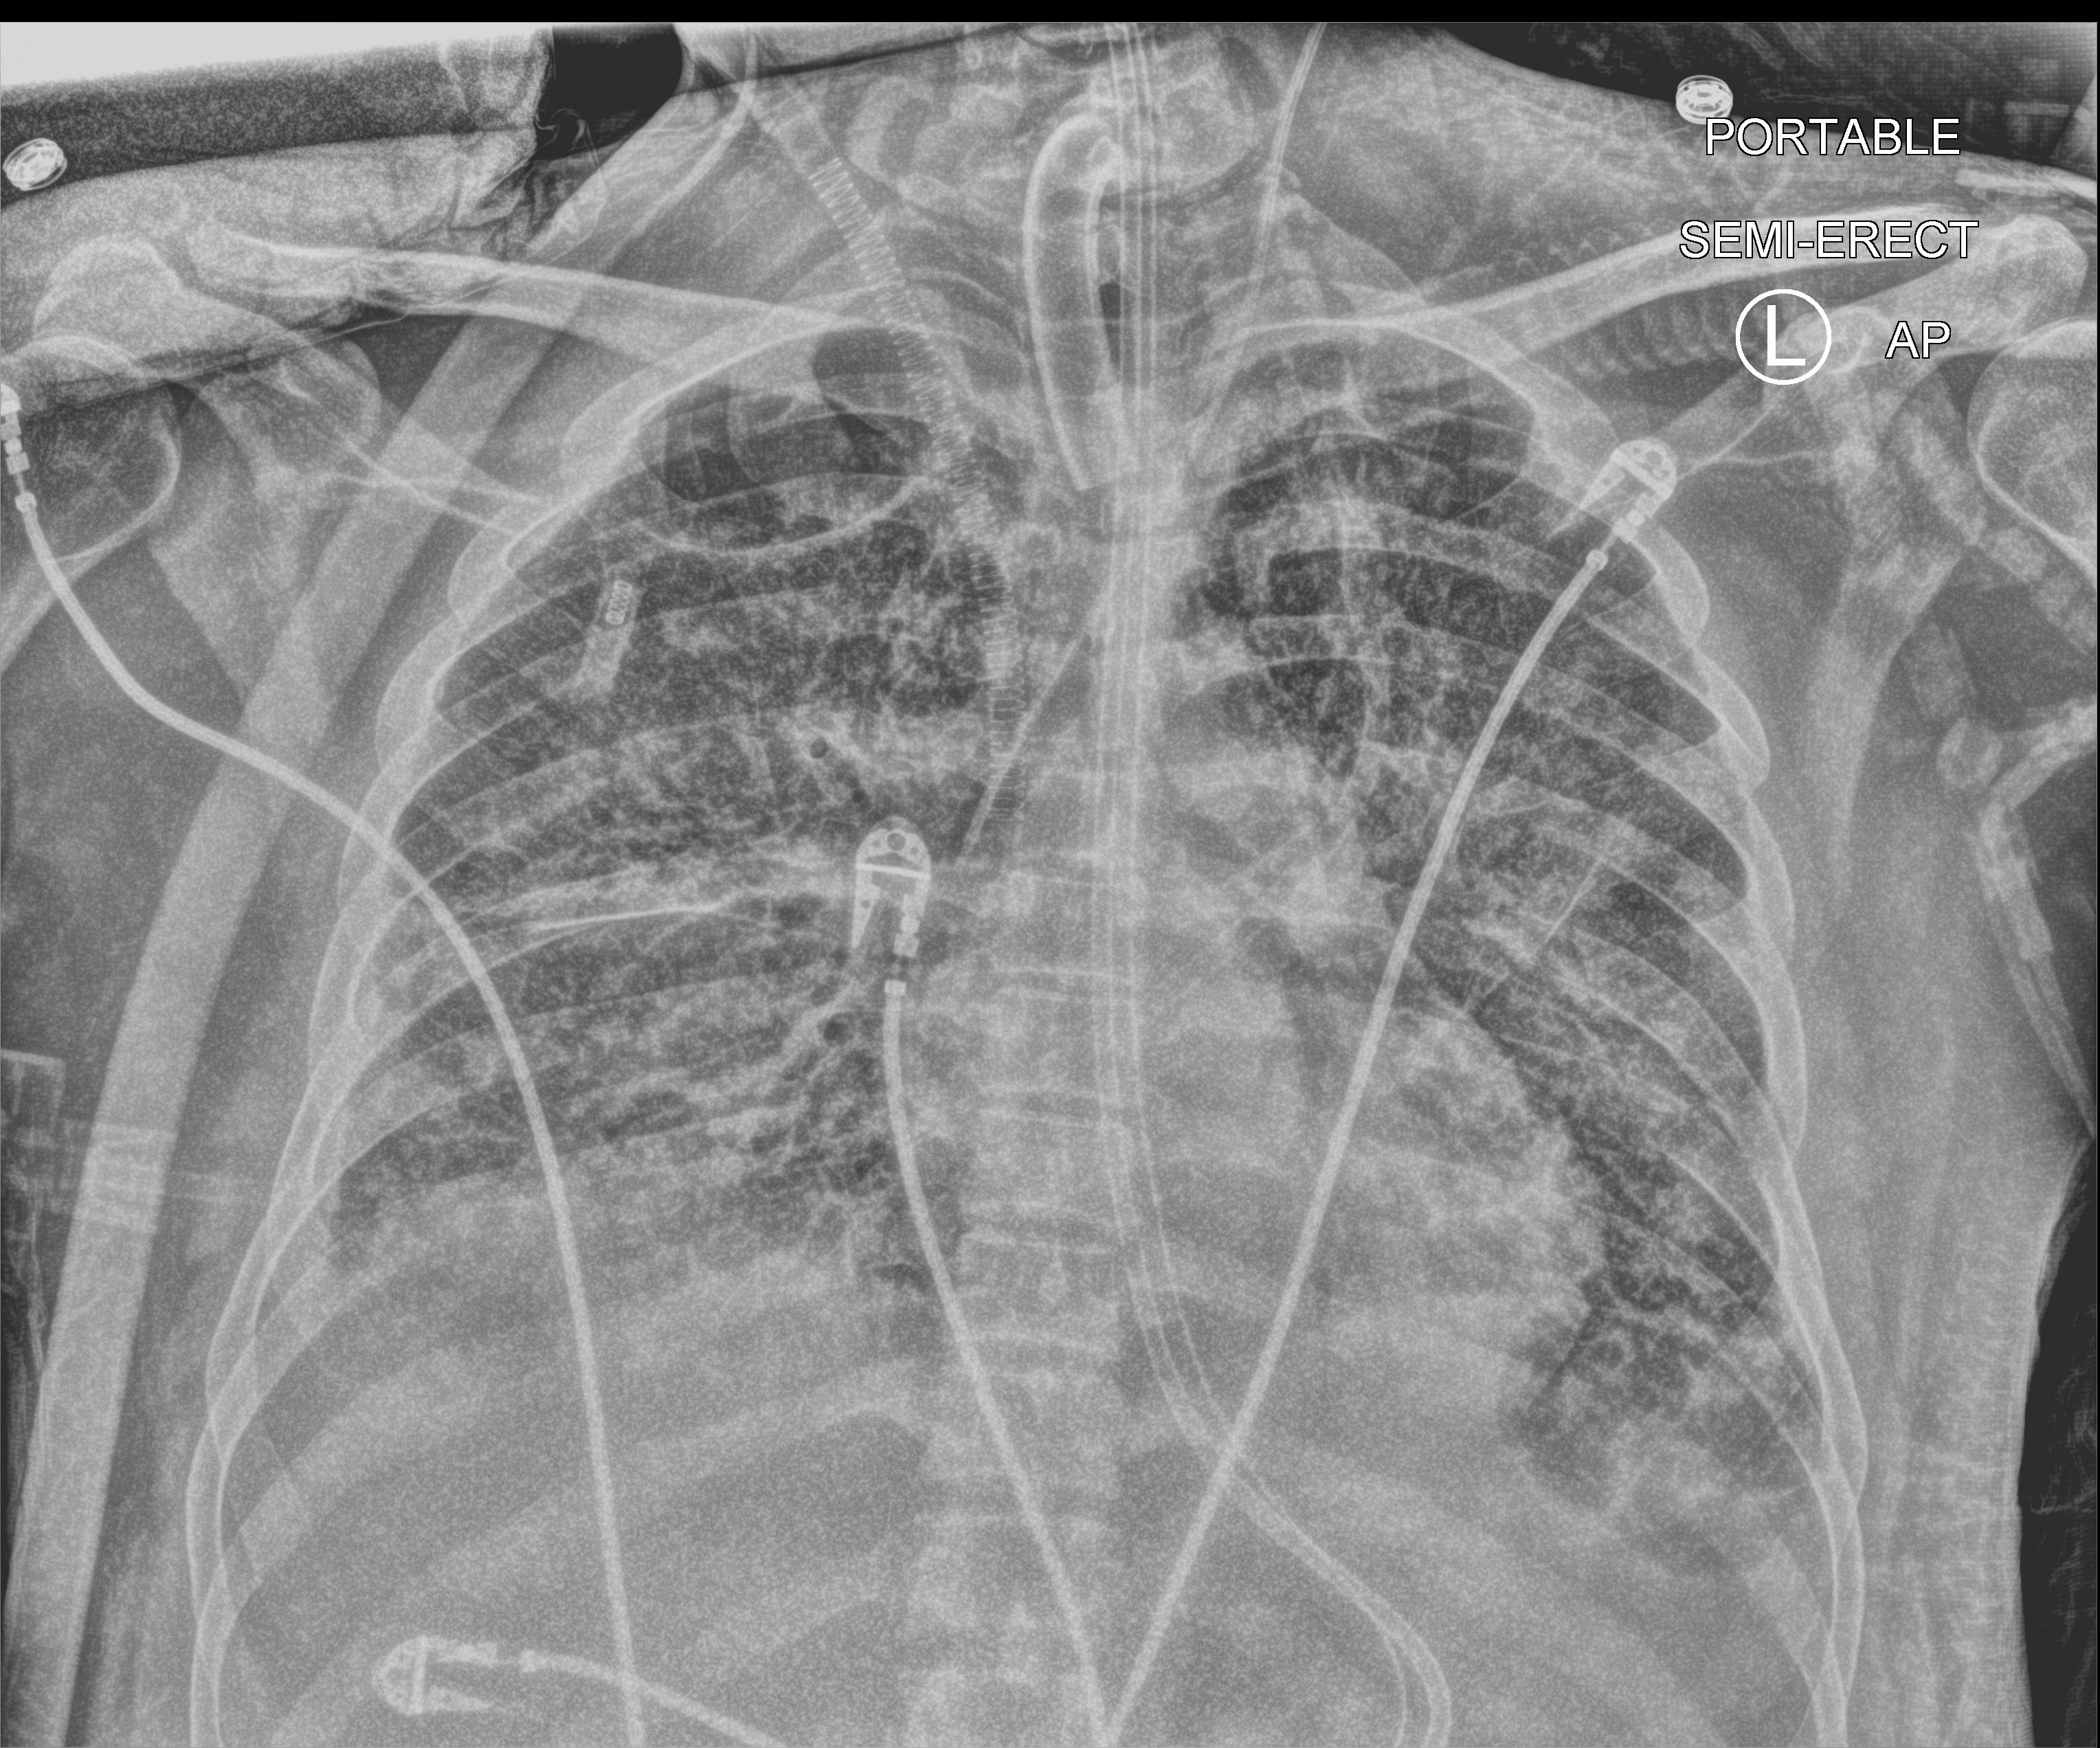
Chest X-ray (portable), anteroposterior (AP) projection. Adult patient hospitalised with COVID-19, age 18–59 years.
Admission-level facts for this patient (not findings on this image; timing relative to this image not recorded):
- admitted to intensive care during this hospital stay: yes
- mechanically ventilated during this hospital stay: yes